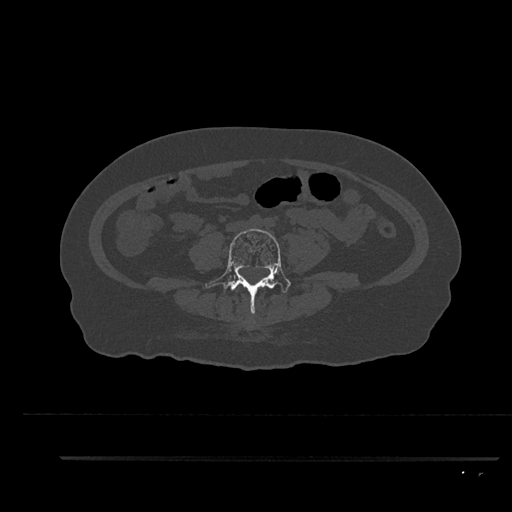
CT including the spine, one axial slice. Slice 25 of 797 in the series (ordered by position). 120 kVp. Bone window (W 1800 / L 400 HU). 0.5 mm slice thickness. 512 × 512 image matrix. Patient: female, 44 years. Case-level facts recorded for this patient, not image findings: primary cancer: renal.
Outlined on this slice (semi-automatic segmentation, software-assisted and operator-edited):
- L4 vertebra: bounding box (x1, y1, x2, y2) in pixels: (206, 229, 291, 316)